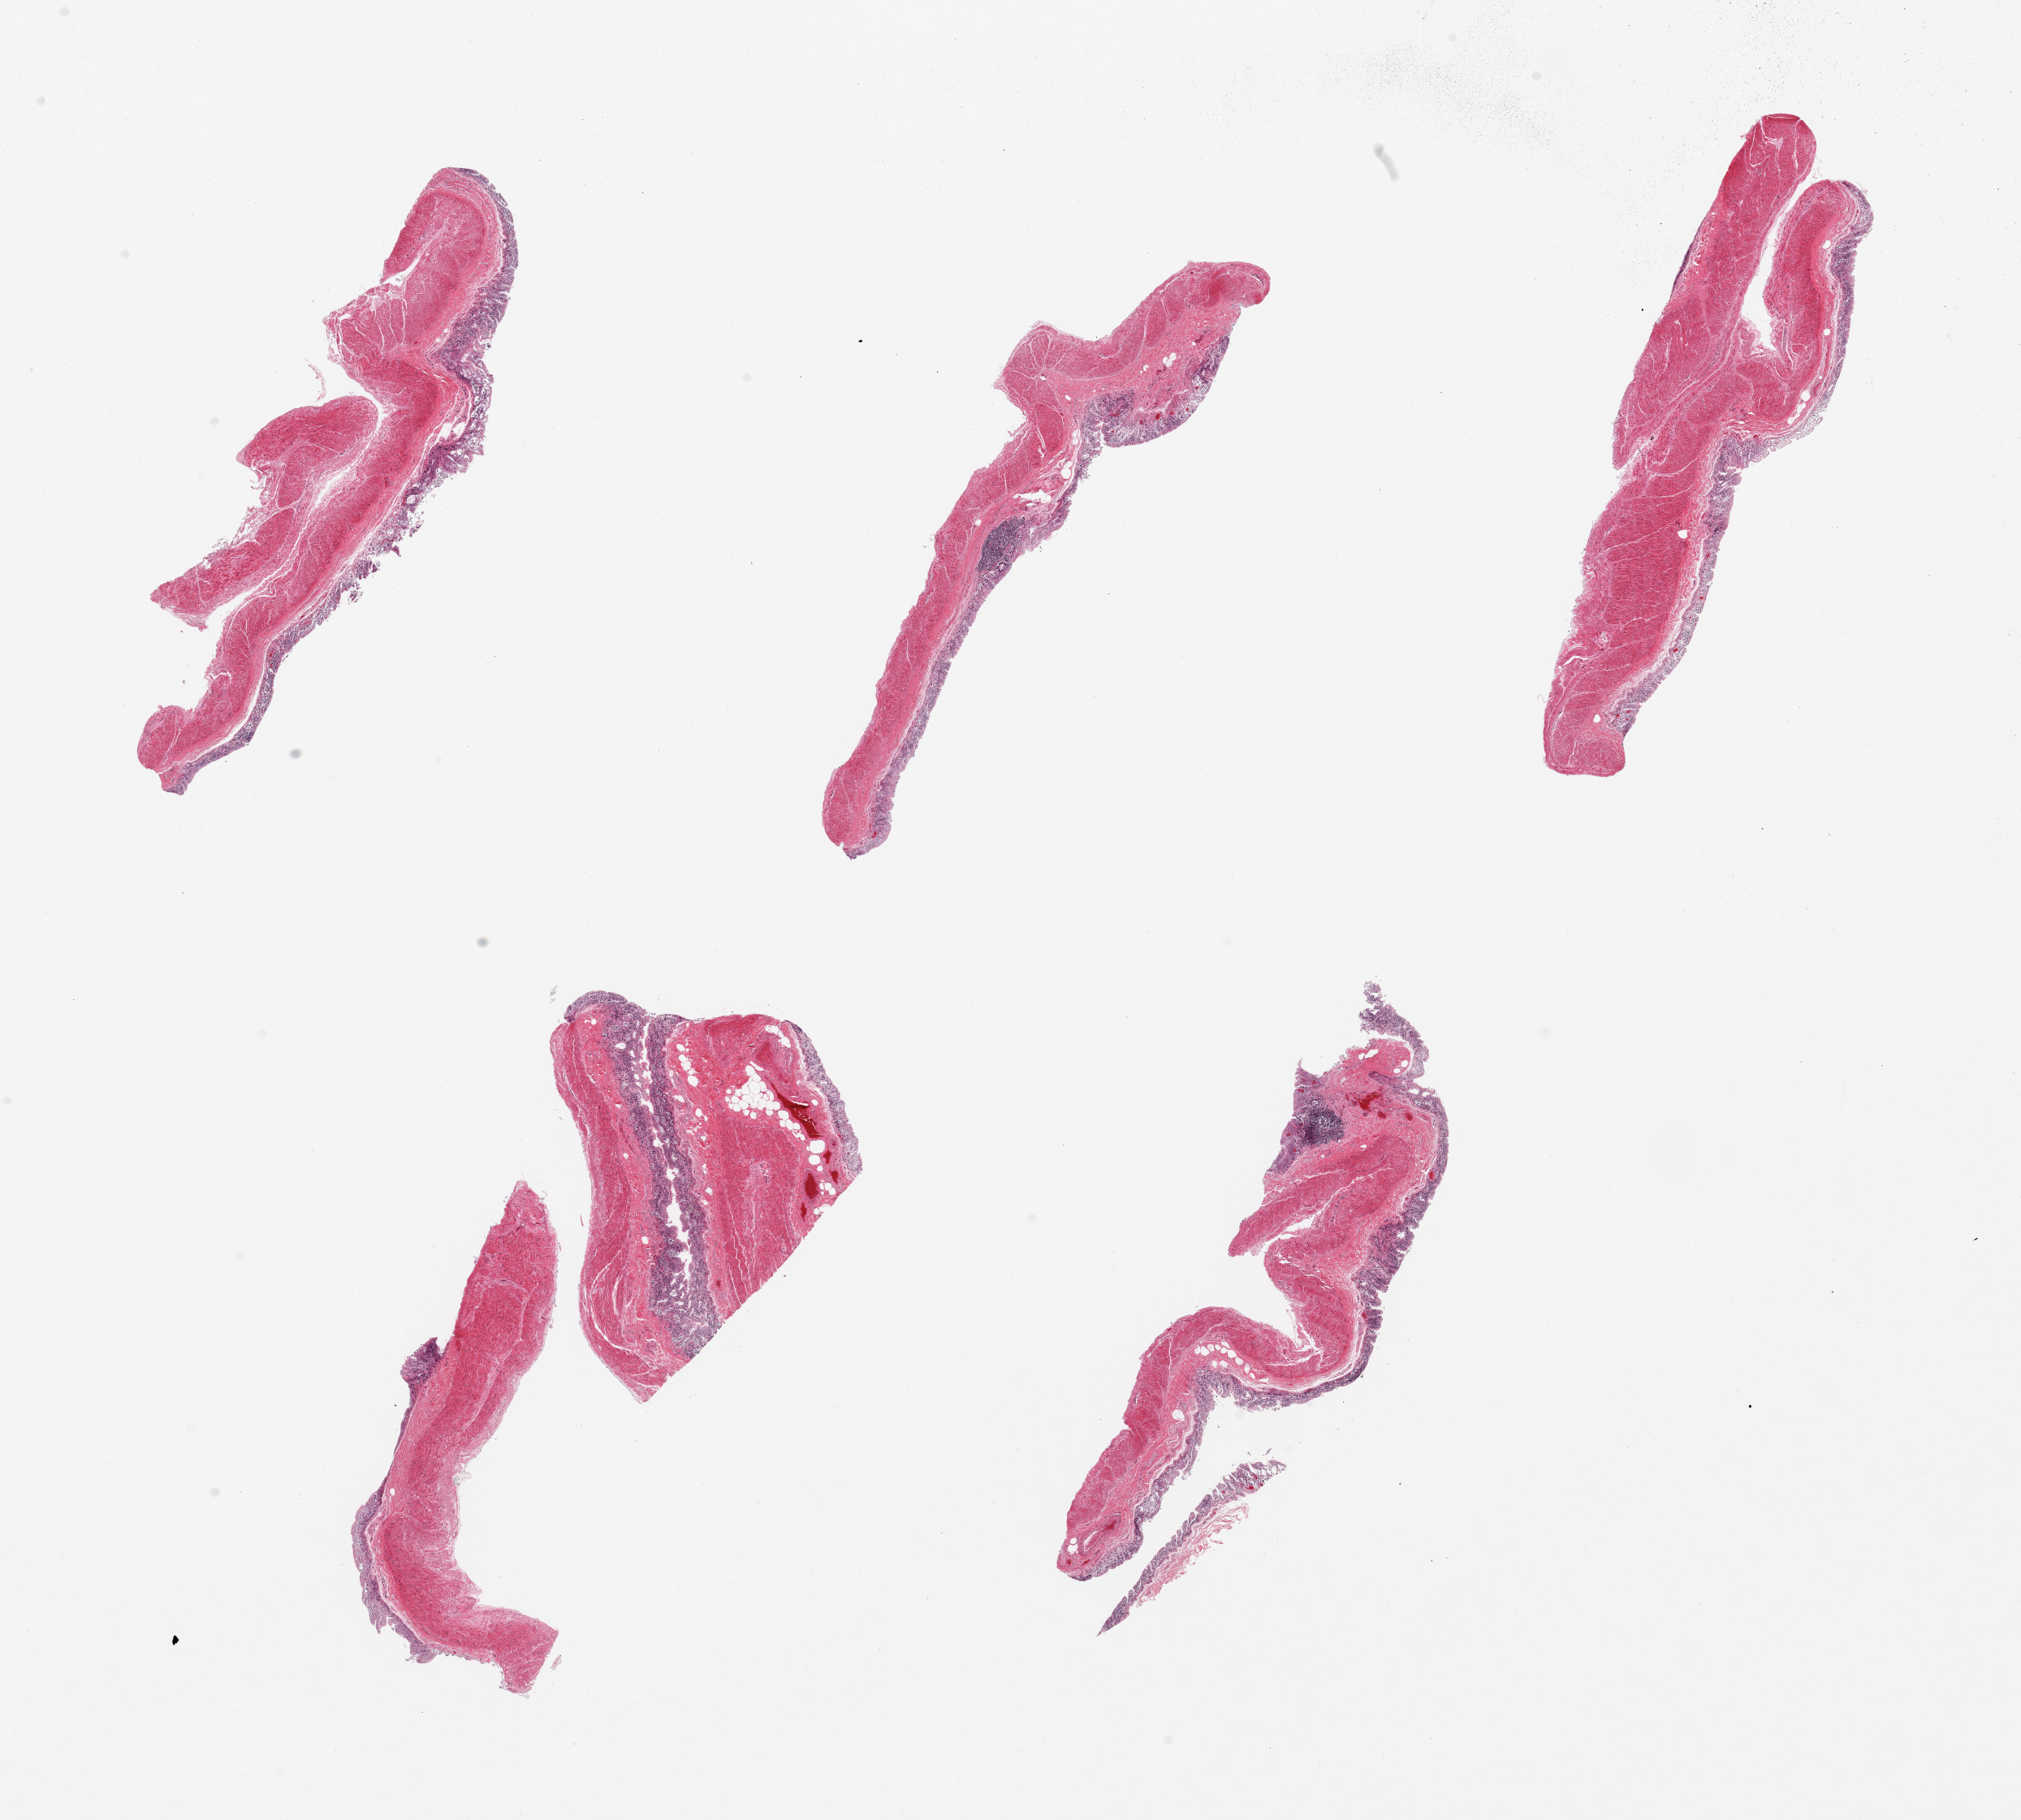
H&E whole-slide image, a low-resolution overview of the entire scanned area, about 19.7 x 17.7 mm (slide scanned at 20x); PAXgene-fixed, paraffin-embedded tissue; section of transverse colon (target tissue); donor tissue sample. Female donor.
- reviewer comment on this tissue sample: 6 pieces; full thickness sections with moderate to severe mucosal autolysis